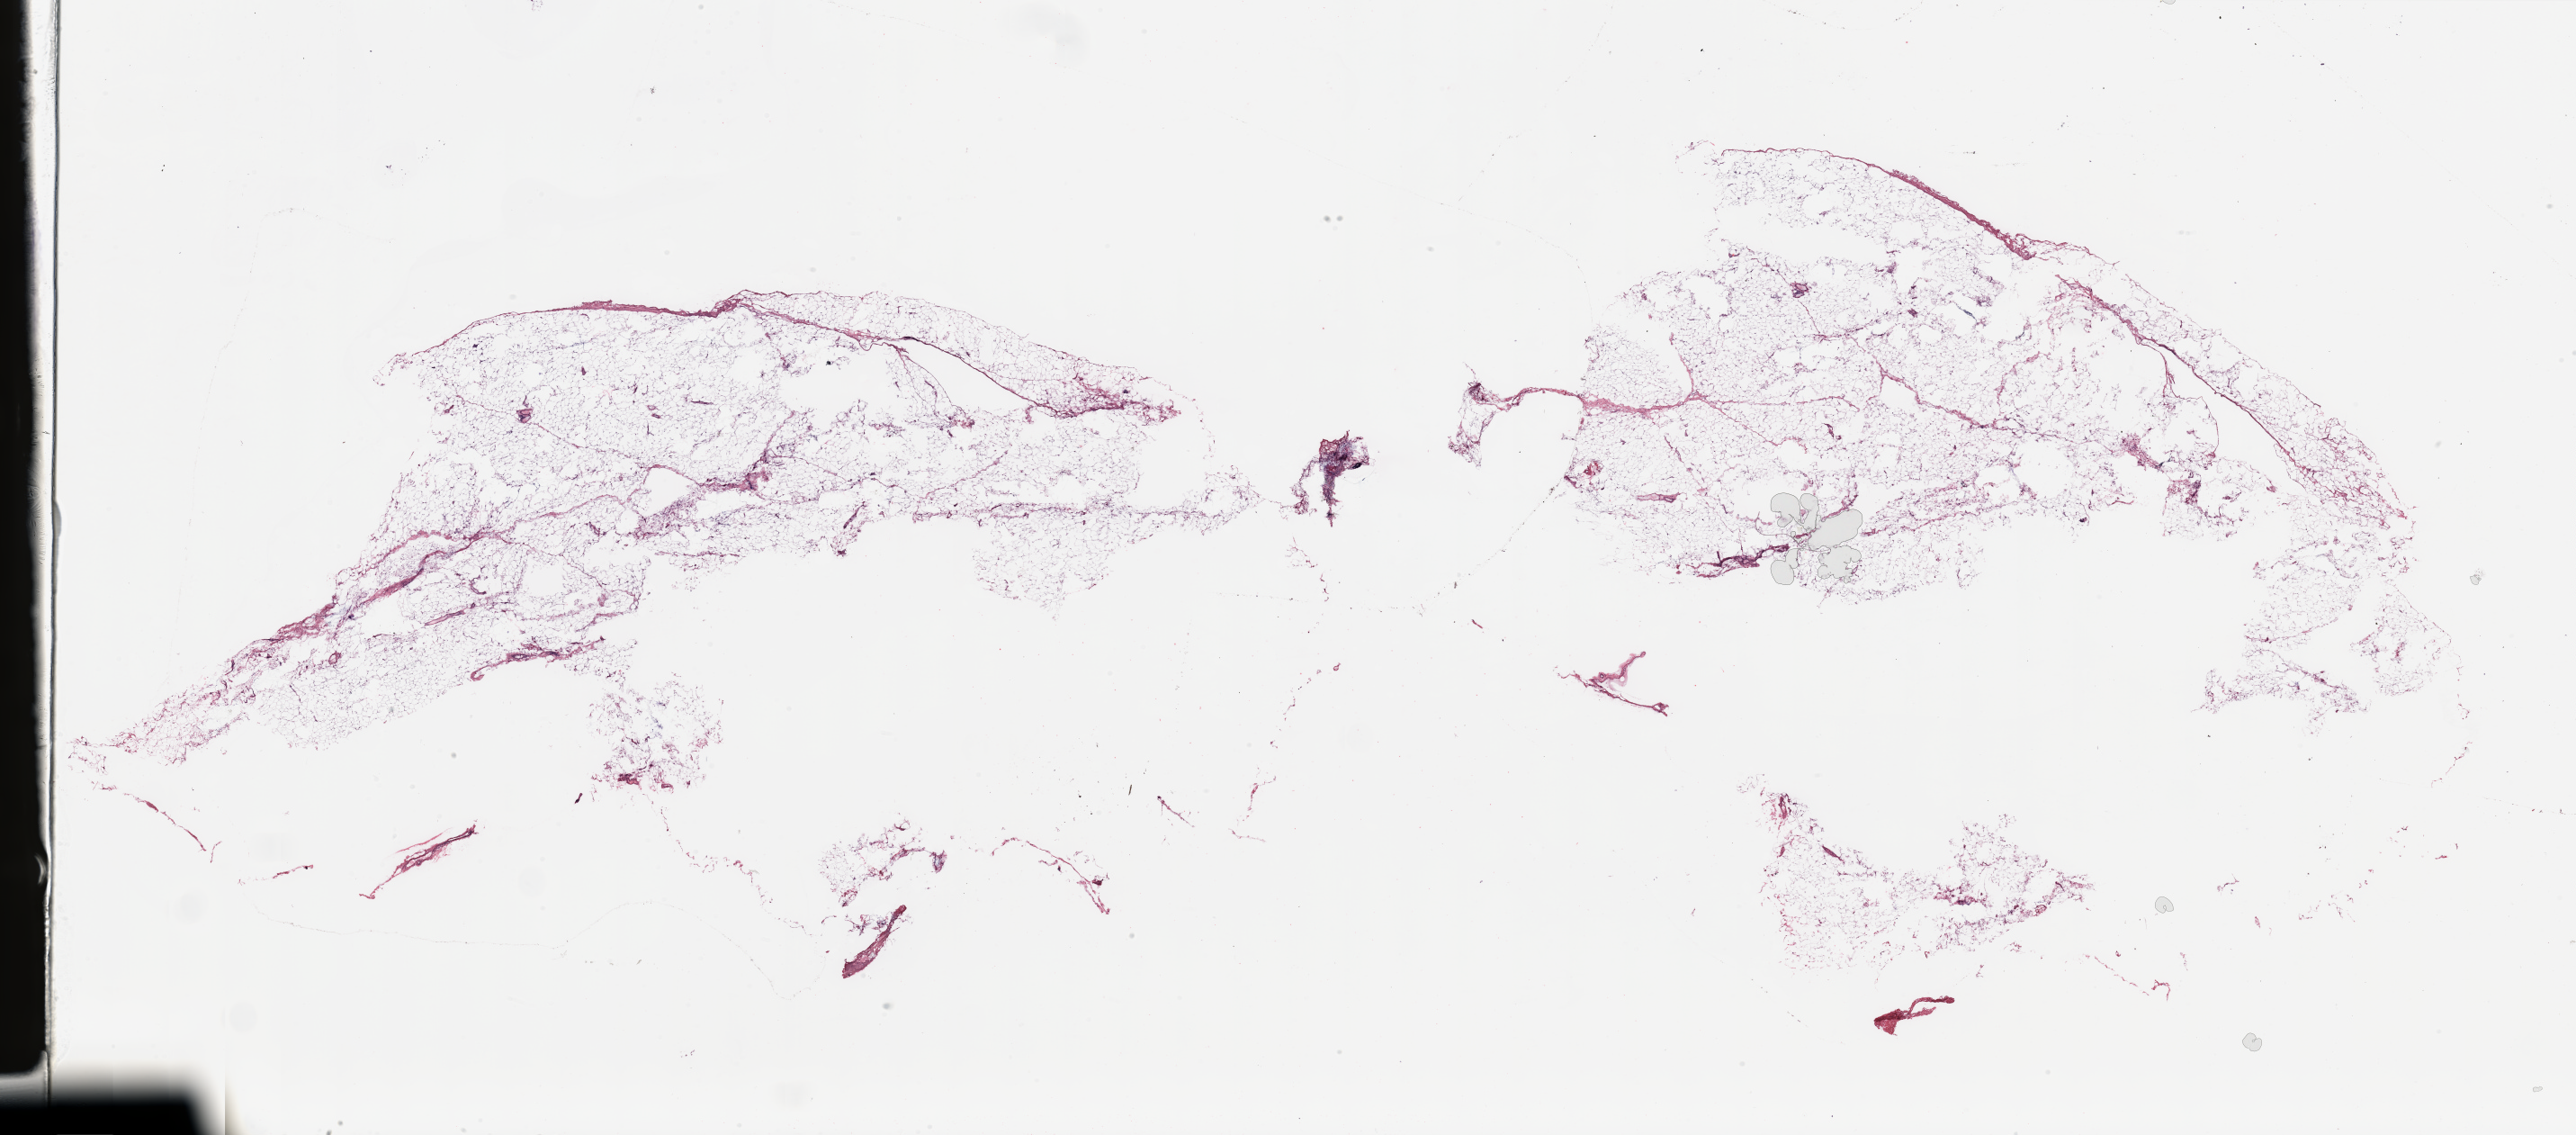
Digitized Hematoxylin and eosin (H&E) stained tissue section (whole slide), low-resolution overview of the scanned area, about 45.3 x 19.9 mm (acquisition: 20x scan), breast, tumour tissue. Patient: female, age 67 years.
Histologic diagnosis: Infiltrating duct carcinoma, NOS.